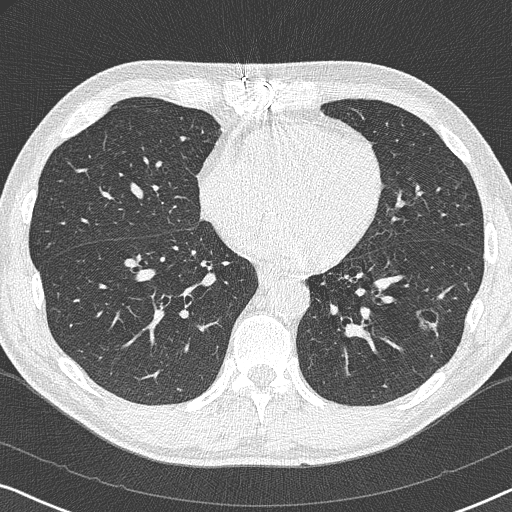
Chest CT (low-dose screening protocol), one axial image, baseline screening round, lung window (W 1500 / L -600 HU), lung (sharp) reconstruction kernel (B50f), slice 211 of 327 in the series. Male participant, aged 59 years at enrolment.
• Lesion marked by an expert reader, bounding box (x1, y1, x2, y2) in pixels: (409, 303, 450, 335).
• The screening reader recorded 2 non-calcified nodules or masses ≥4 mm on this exam; which of them this box marks is not recorded.
• Lung cancer was diagnosed 821 days after this screen (after the third annual screen): adenocarcinoma, NOS, left lower lobe, poorly differentiated (G3), stage IA (AJCC 6th edition), 20 mm at pathology.